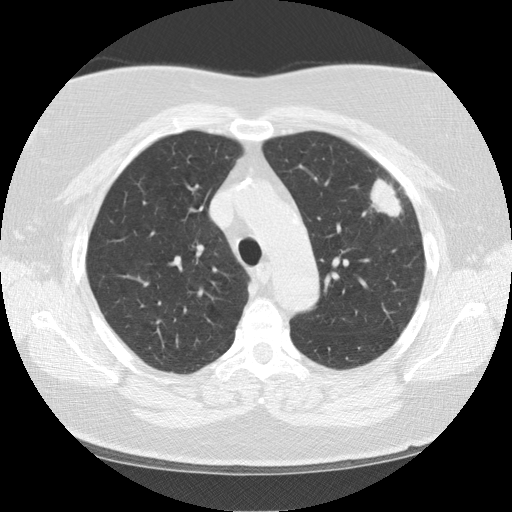
Chest CT (low-dose screening protocol), one axial image. Baseline annual screen. Lung window (W 1500 / L -600 HU). Standard (soft-tissue) reconstruction kernel (STANDARD). Slice 35 of 130 in the series. Female, age 67 years at enrolment. Former smoker at enrolment.
Expert-annotated lung lesion, box from (x=348, y=159) to (x=421, y=228) px. The exam's reader record, not a measurement of the box and not confirmed to be the same lesion: non-calcified nodule or mass ≥4 mm, left upper lobe, 28 × 19 mm, soft tissue attenuation. Official screen result: positive, change unspecified: nodule(s) >= 4 mm or enlarging nodule(s), mass(es), or other non-specific abnormalities suspicious for lung cancer. Lung cancer was diagnosed 33 days after this screen: squamous cell carcinoma, NOS, left upper lobe, poorly differentiated (G3), stage IA (AJCC 6th edition), 25 mm at pathology.